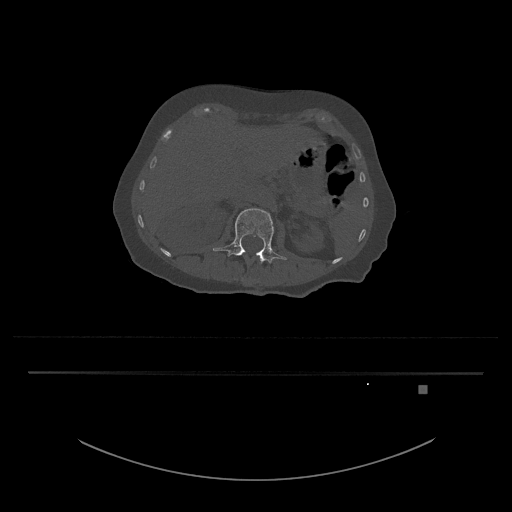
CT including the spine, one axial slice; bone window (W 1800 / L 400 HU); 0.5 mm slice thickness; 512 × 512 image matrix, field of view 500 × 500 mm. Patient: female, 57 years. From the clinical record (not read from this slice): primary cancer: cervical.
Structures marked on this image (semi-automatically segmented with operator editing):
- L1 vertebra: bounding box <257,255,265,262> (left, top, right, bottom; pixels)